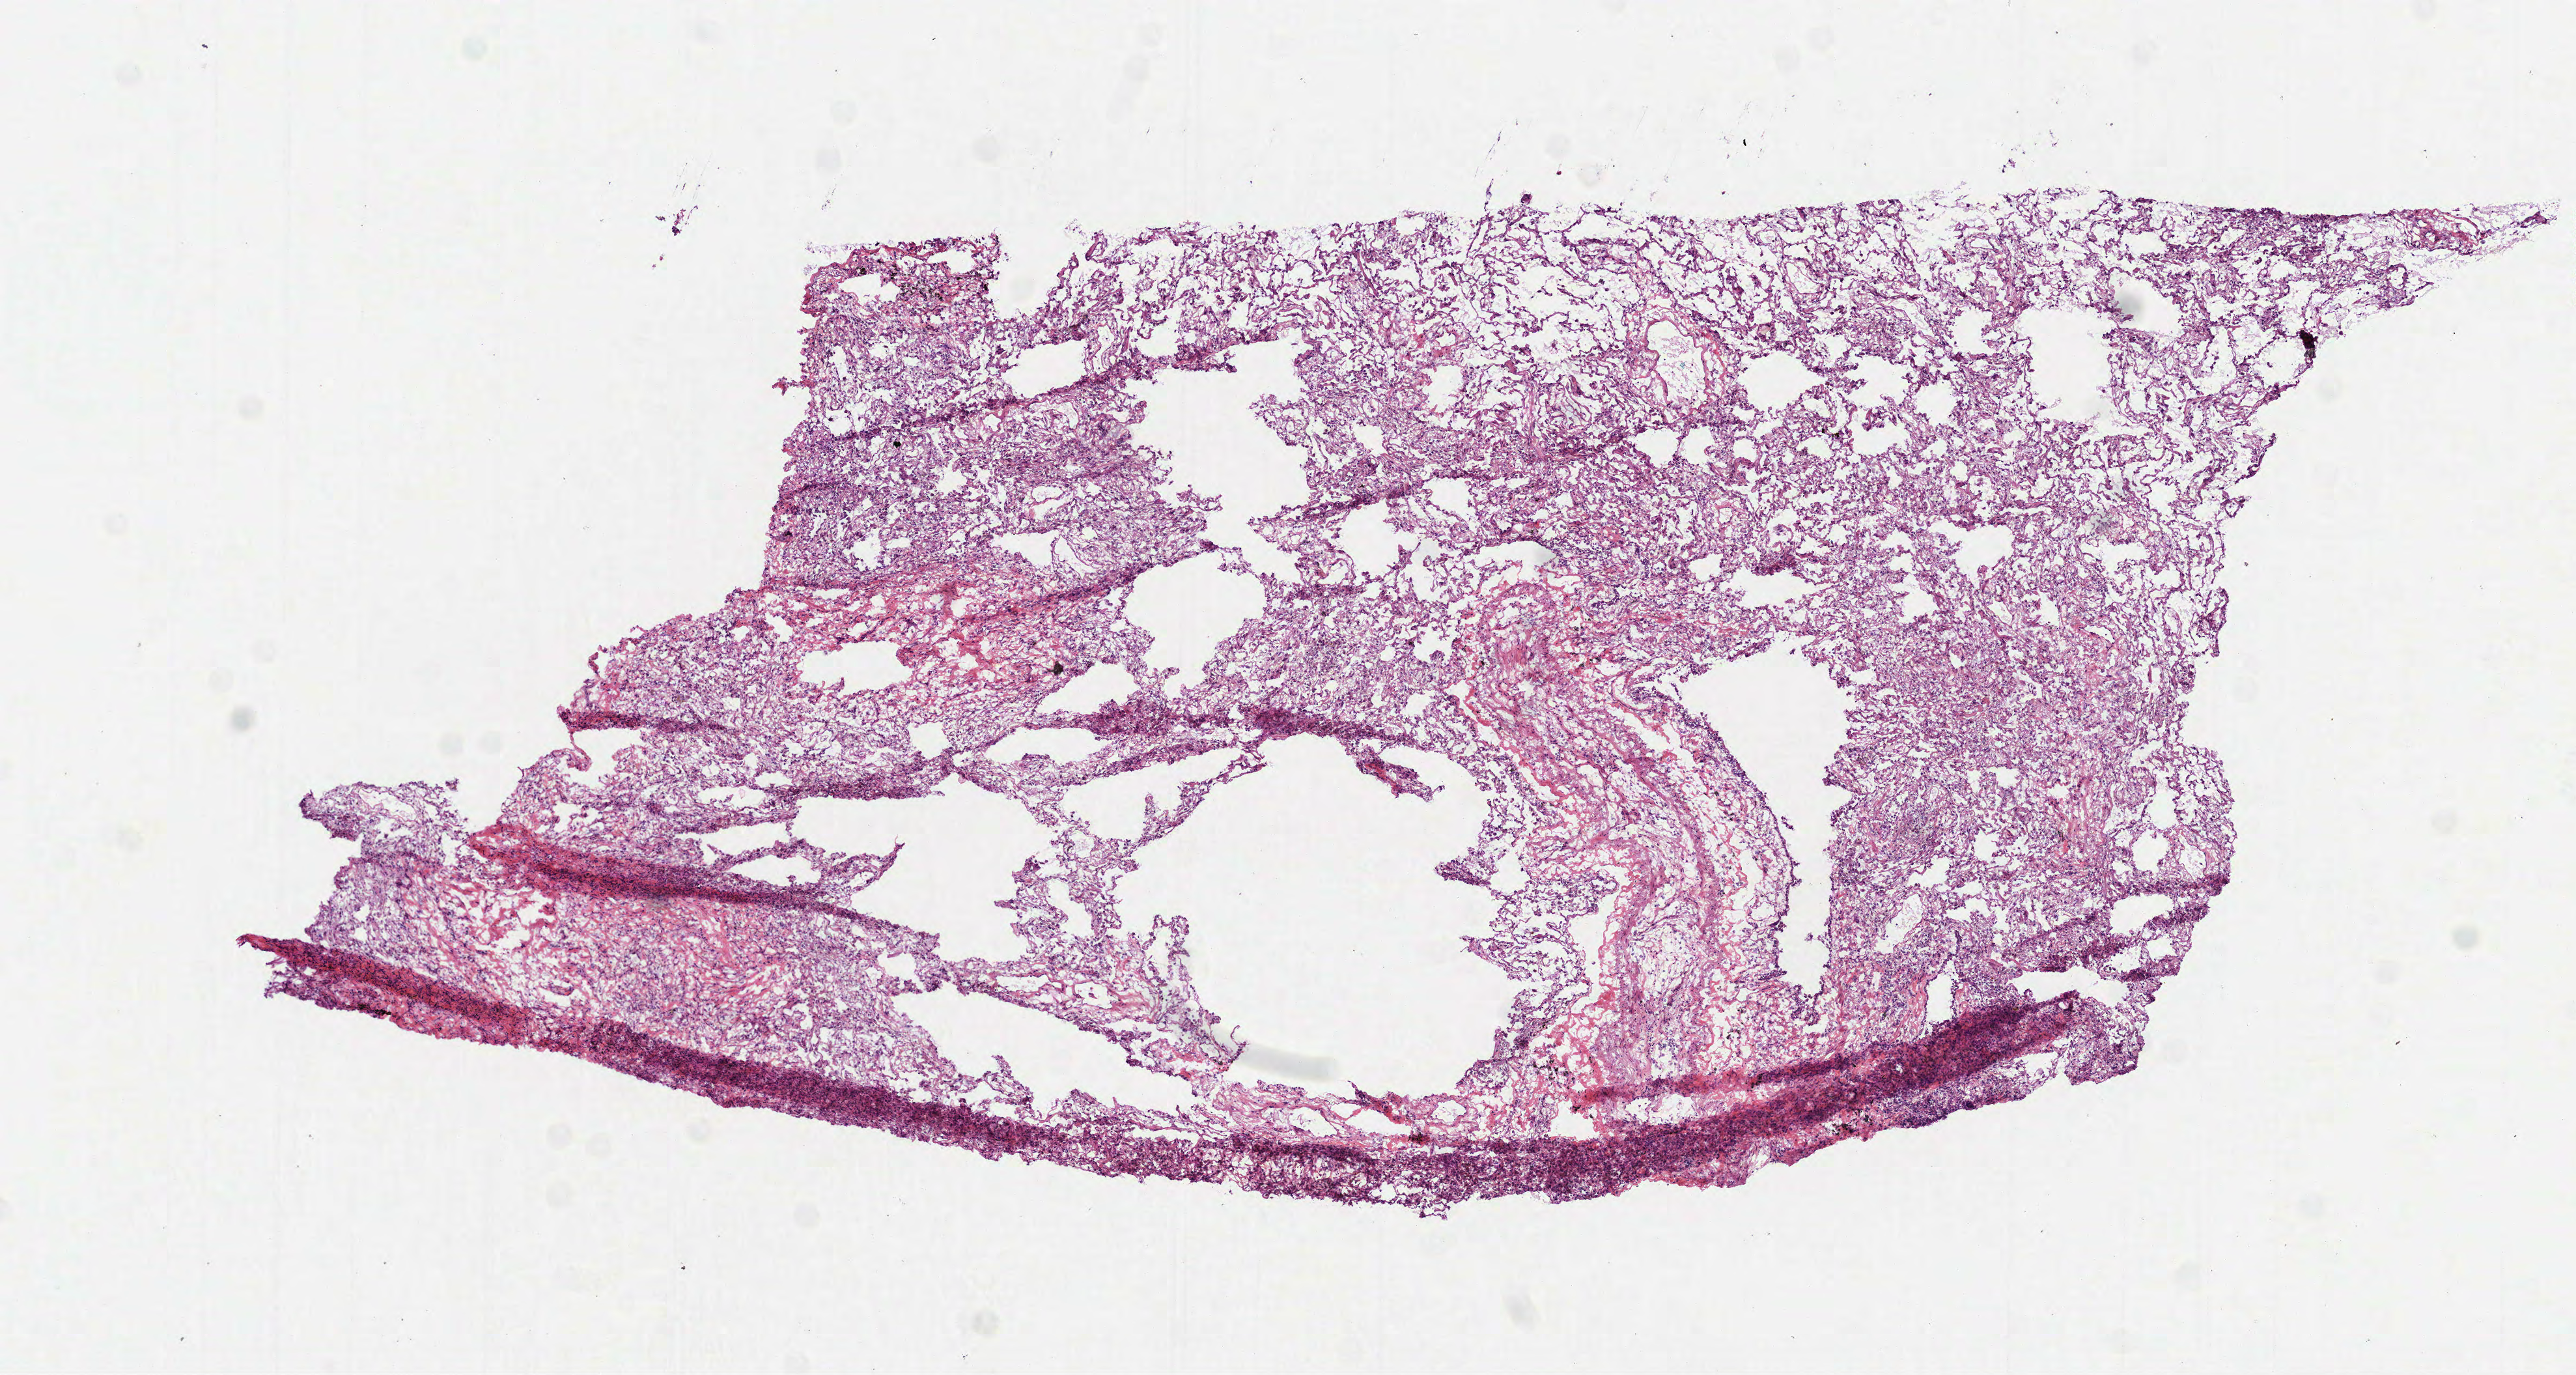
H&E-stained whole-slide image, a low-resolution overview of the entire scanned area, about 8.0 x 4.3 mm (acquisition: 40x scan), frozen section from the top of the tissue portion, sample: solid tissue normal (non-tumour tissue), lung. Male, age 83 years at initial diagnosis.
* this section: solid tissue normal sample (biorepository sample class)
* patient diagnosis: Squamous cell carcinoma, NOS (lower lobe, lung)